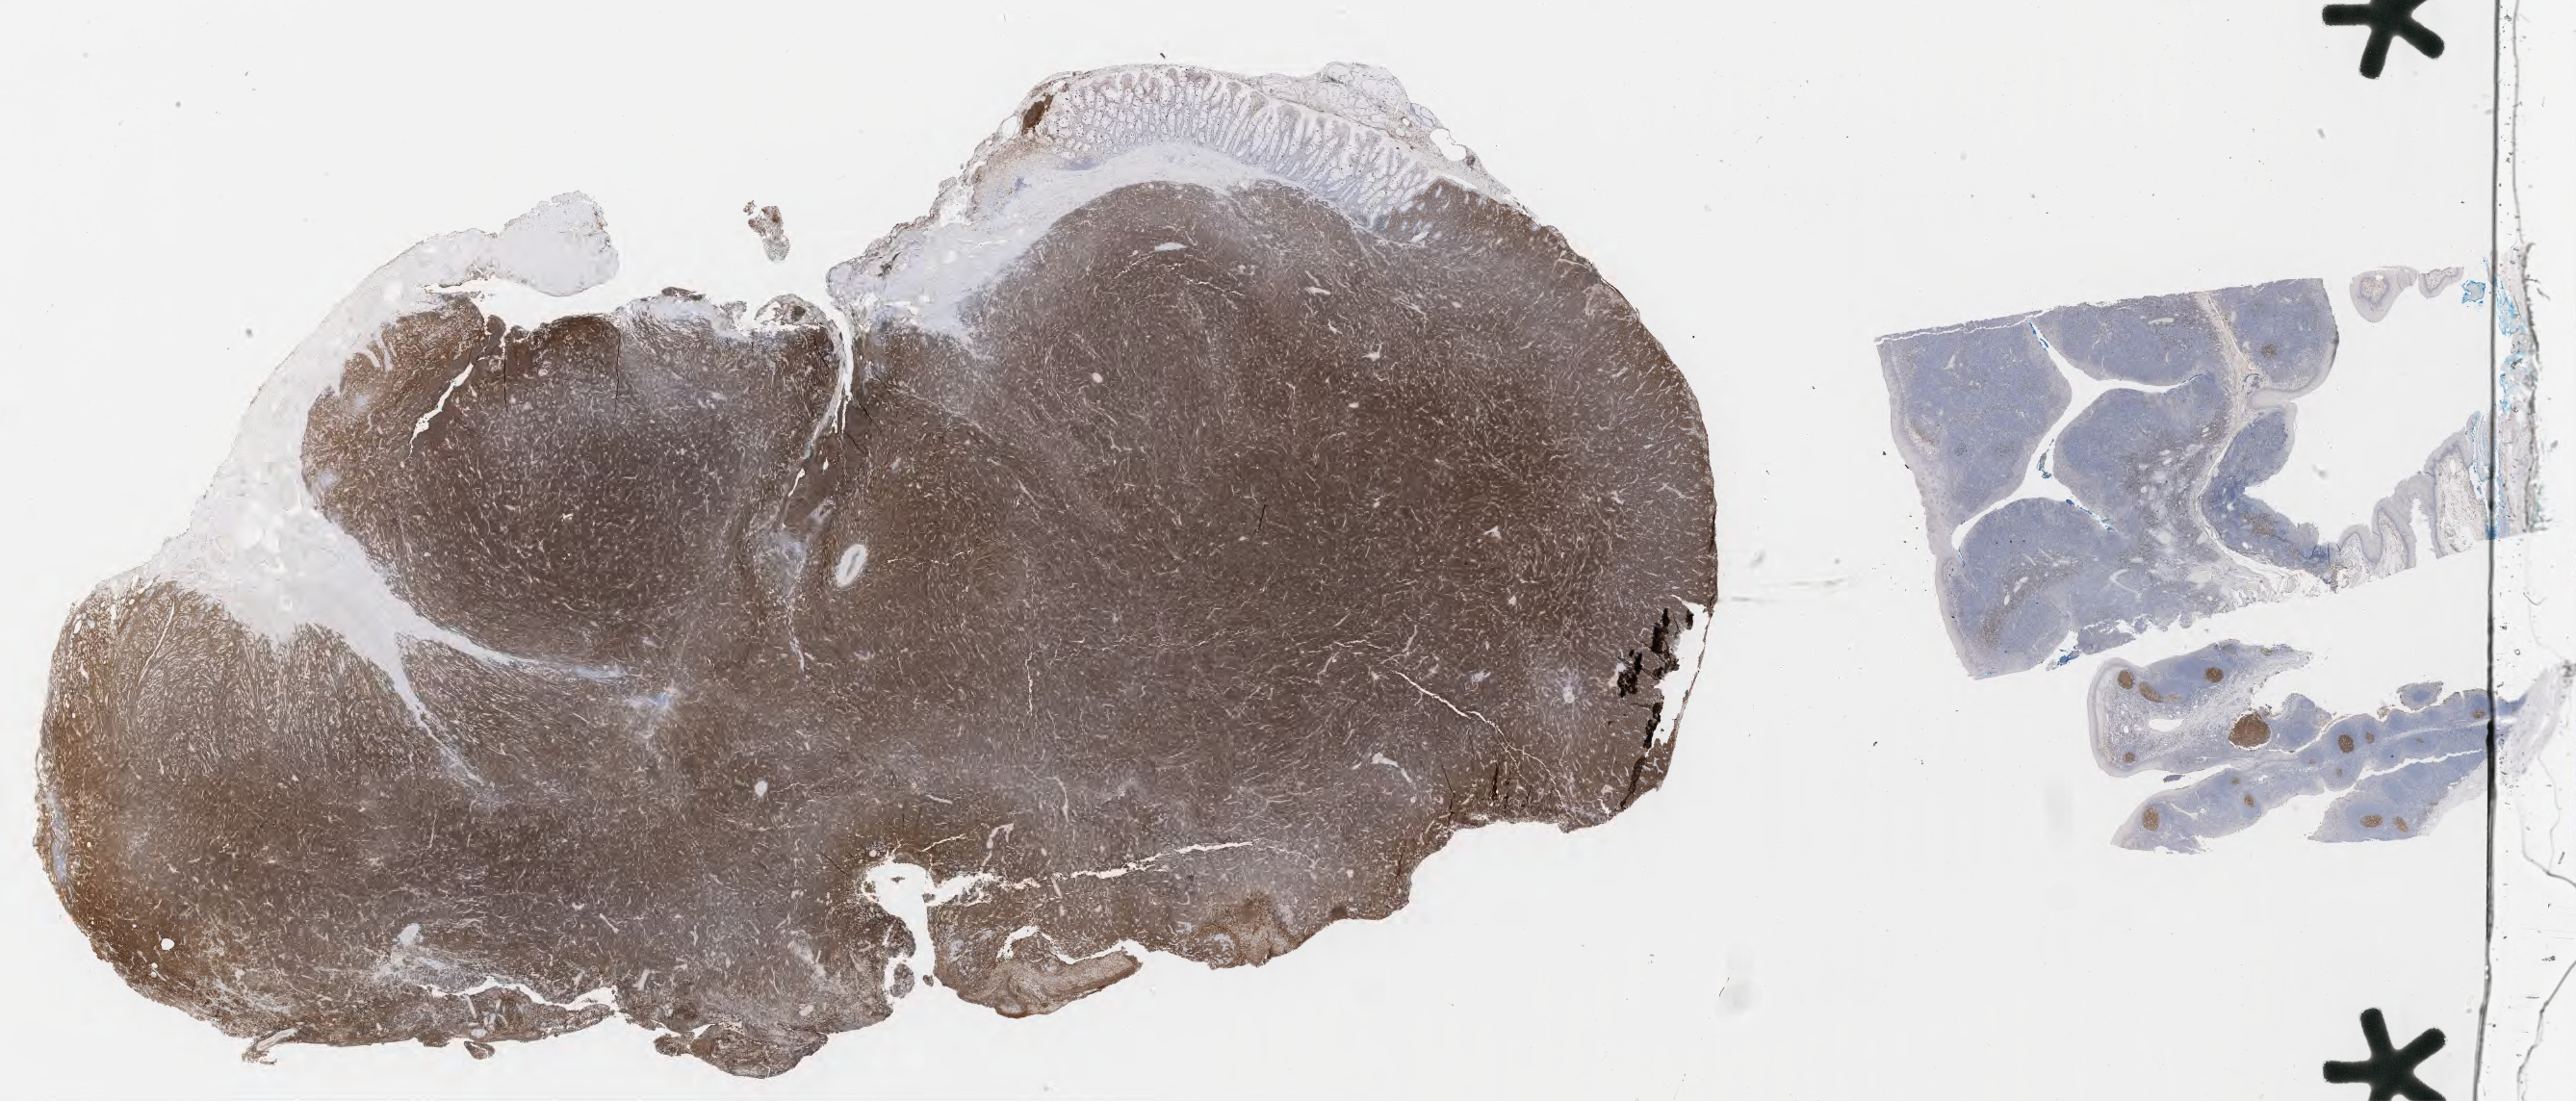
Immunohistochemistry (IHC) whole-slide image stained for CD10, low-resolution overview of the scanned area, about 43.3 x 18.5 mm. Tumor tissue. Patient: female, aged 29.
Histologic diagnosis: Burkitt lymphoma, NOS.